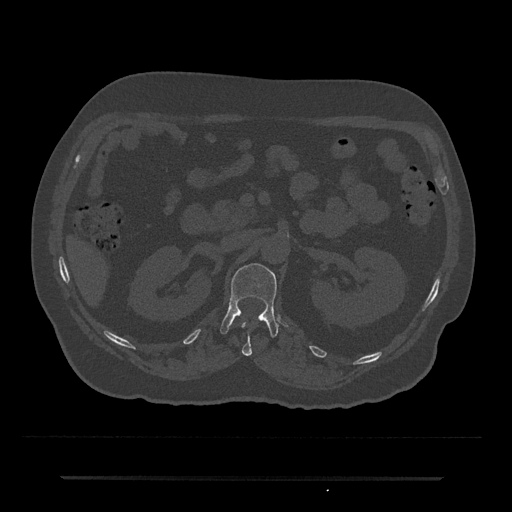
CT including the spine, one axial slice. Position 86 of 797 along the scan axis. Reconstruction kernel Br40s/3. Bone window (W 1800 / L 400 HU). 512 × 512 image matrix, field of view 437 × 437 mm. Male patient, age 69 years. From the clinical record (not read from this slice): primary cancer: prostate.
Structures marked on this image (semi-automatic segmentation, software-assisted and operator-edited):
- L1 vertebra: box from (x=220, y=263) to (x=278, y=338) px
- T12 vertebra: (x=241, y=322)–(x=252, y=356)